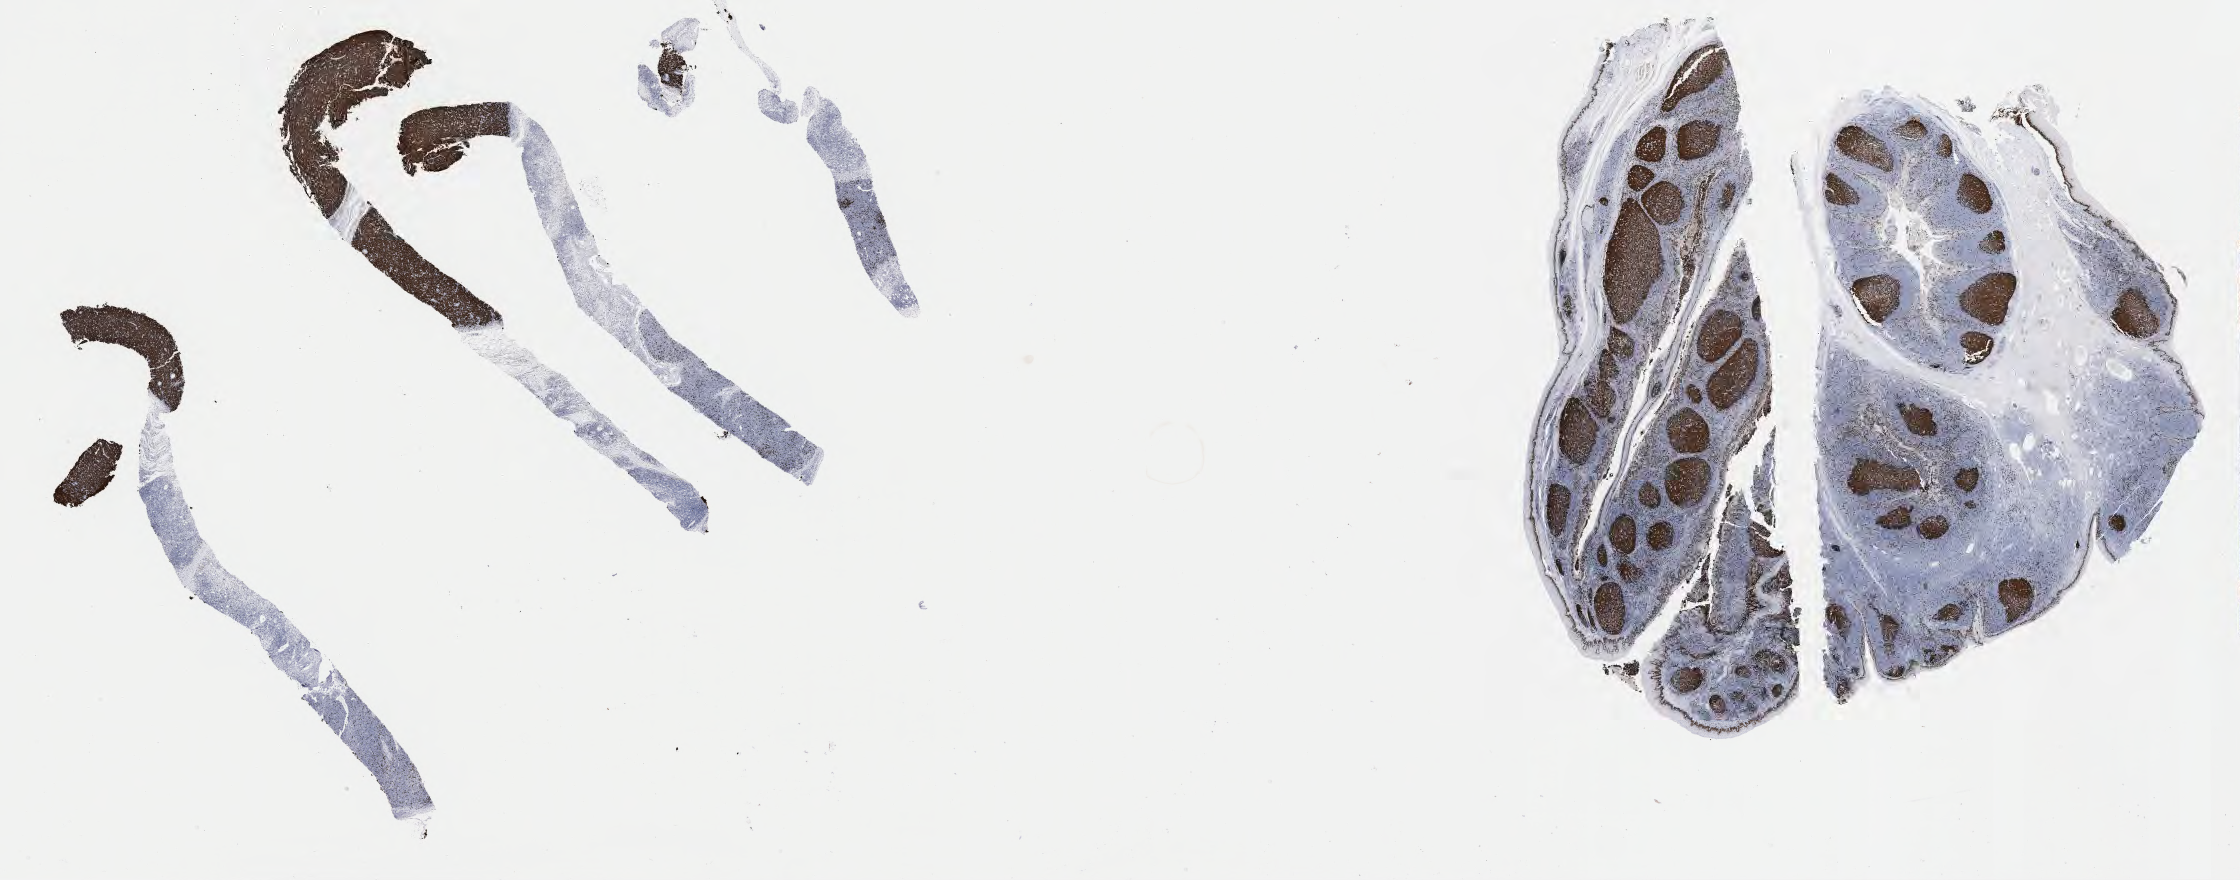
Immunohistochemistry (IHC) whole-slide image stained for Ki-67 — whole scanned area (about 36.2 x 14.2 mm) shown as a low-resolution overview; specimen: tumor tissue. Patient: male, age 47 years.
Histologic diagnosis: Burkitt lymphoma, NOS.